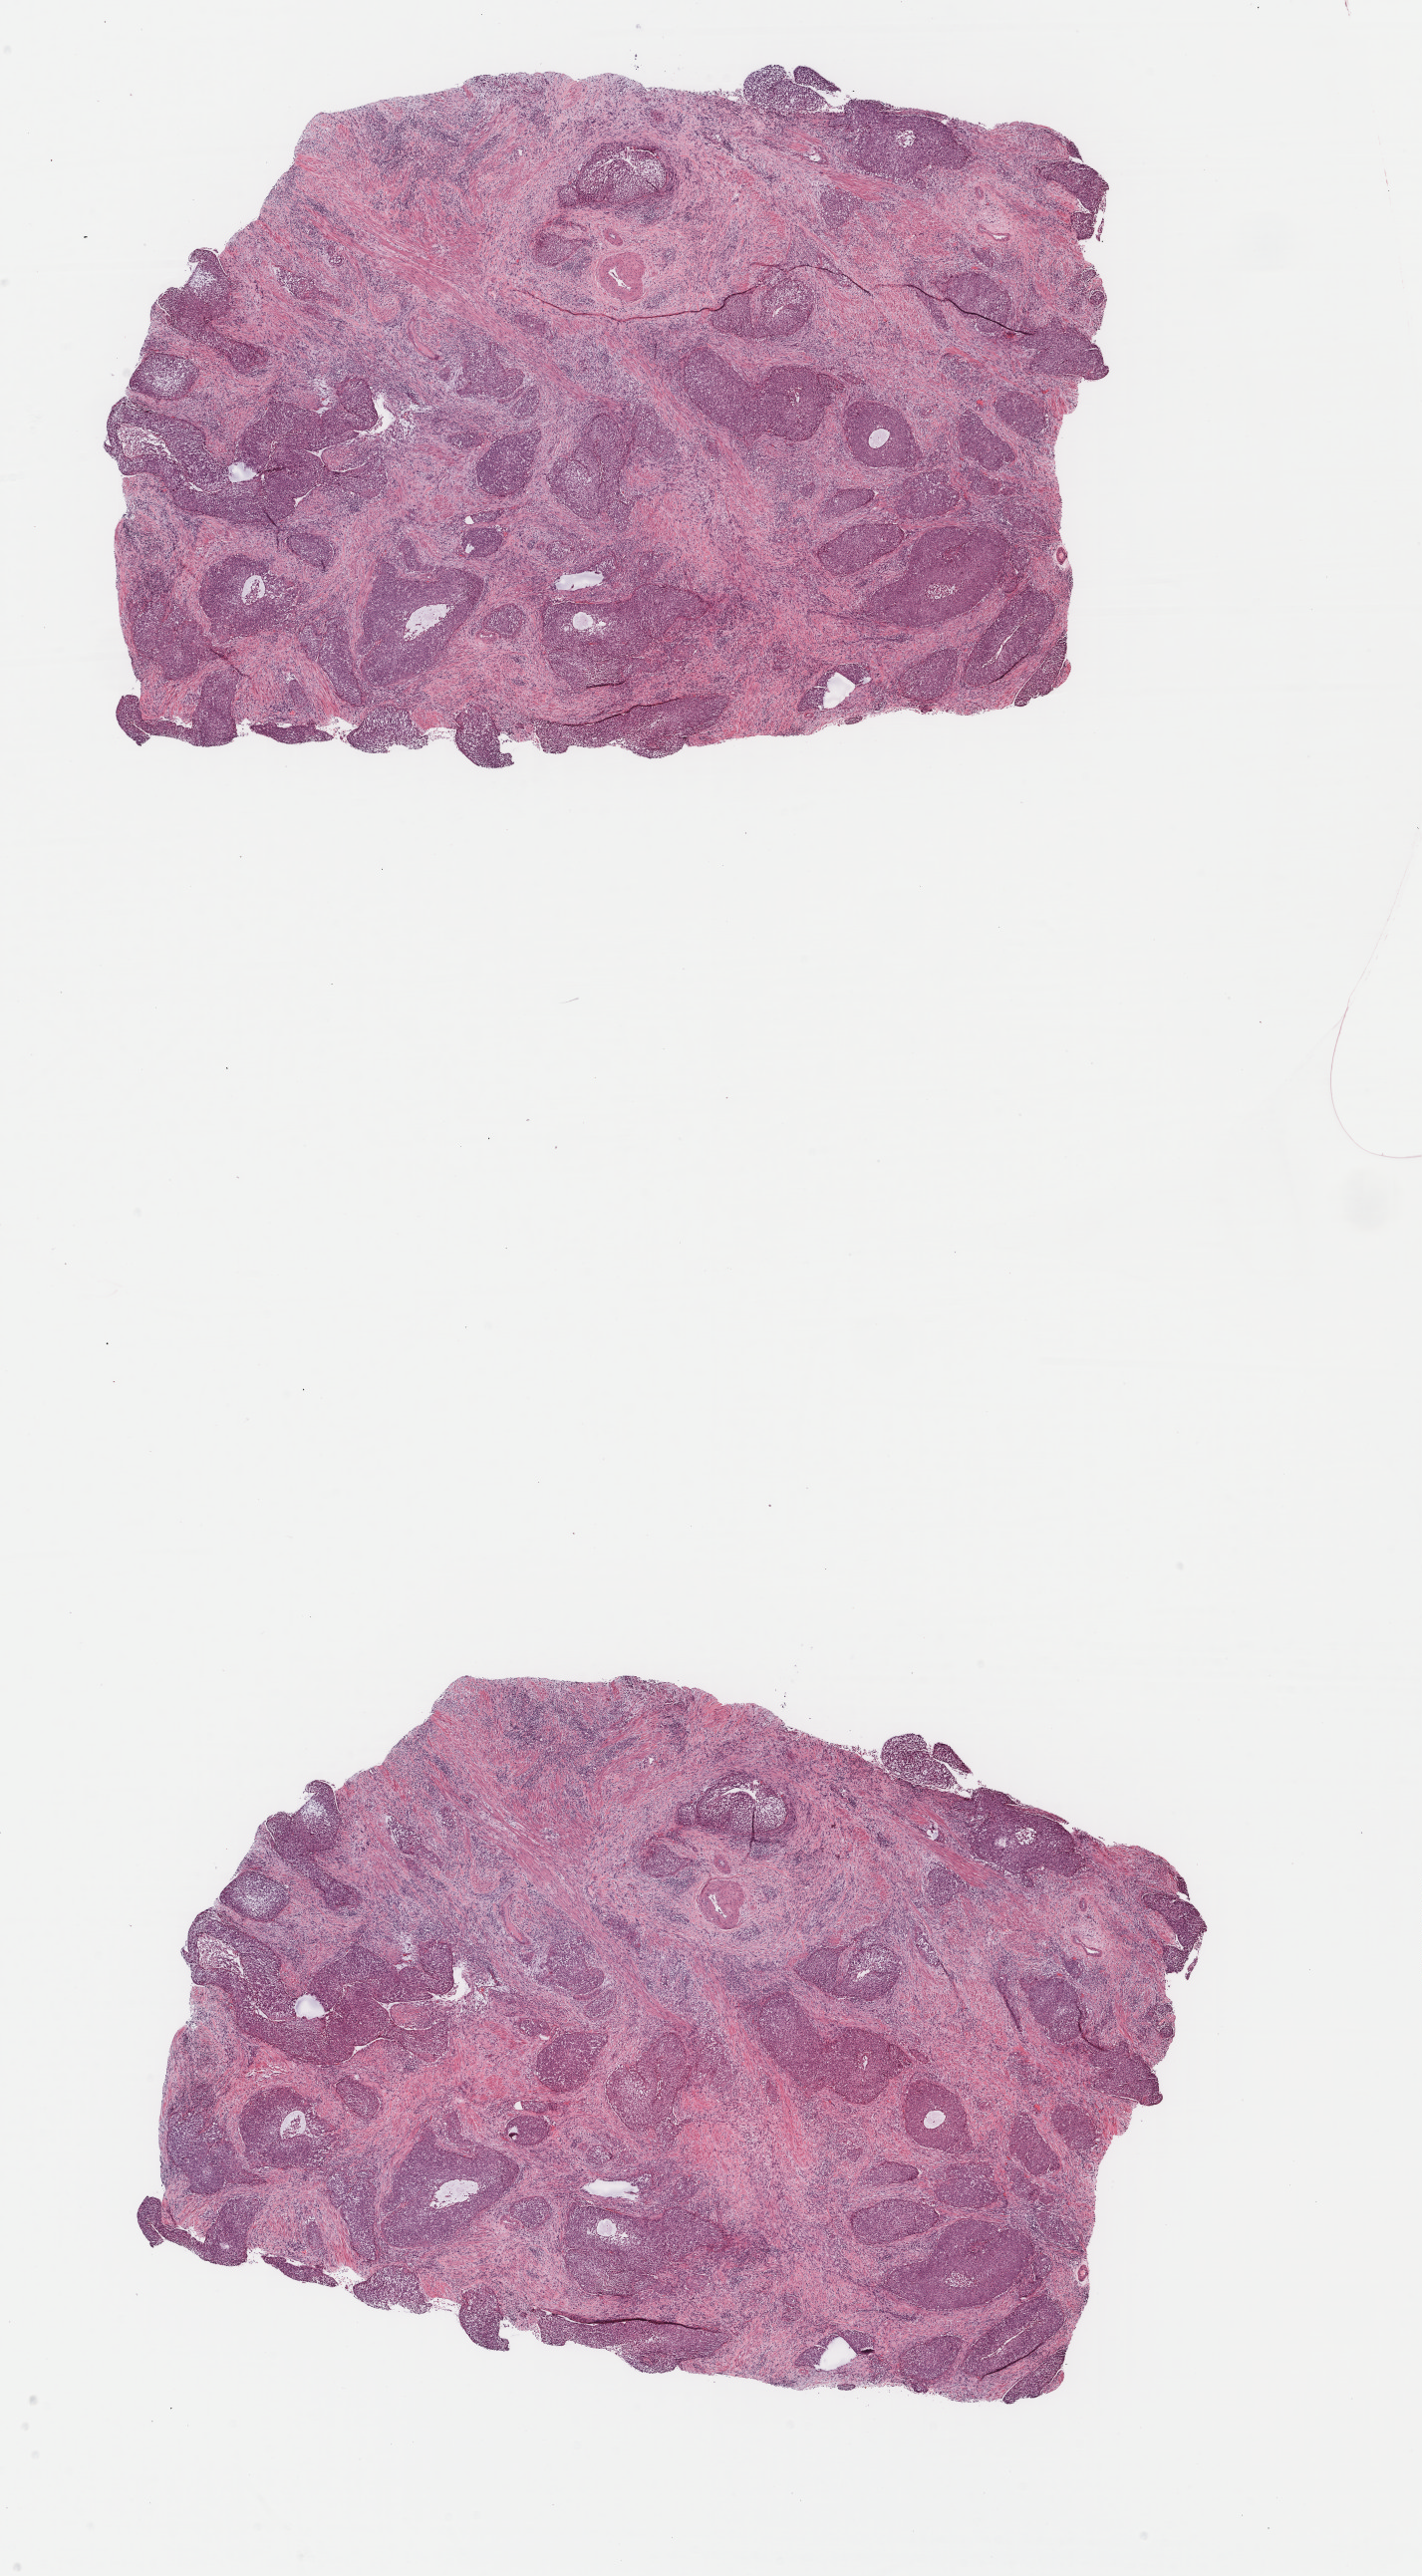
Digitized H&E tissue section (whole slide) — shown as a low-resolution overview of the whole scanned area (about 11.3 x 20.5 mm, acquisition: 40x scan), formalin-fixed paraffin-embedded (FFPE) diagnostic section, cervix, primary tumour sample. Patient: female, age at initial diagnosis 51 years. Histologic grade: G3 (poorly differentiated).
Diagnosis: Squamous cell carcinoma, NOS (cervix uteri). FIGO stage: IIIB.